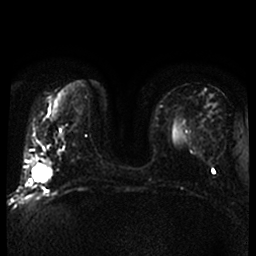
Breast MRI, one axial slice; slice 13 of 52 in the series (ordered by position); diffusion-weighted series; image 2 of 4 stored at this slice position (different b-values; order by instance number); 1.5 T; 4 mm slice thickness; 256 × 256 image matrix. Female patient.
Annotated regions visible in this slice (outlined manually by an expert reader):
- tumour on diffusion-weighted imaging: bounding box <32,164,52,183> (left, top, right, bottom; pixels)